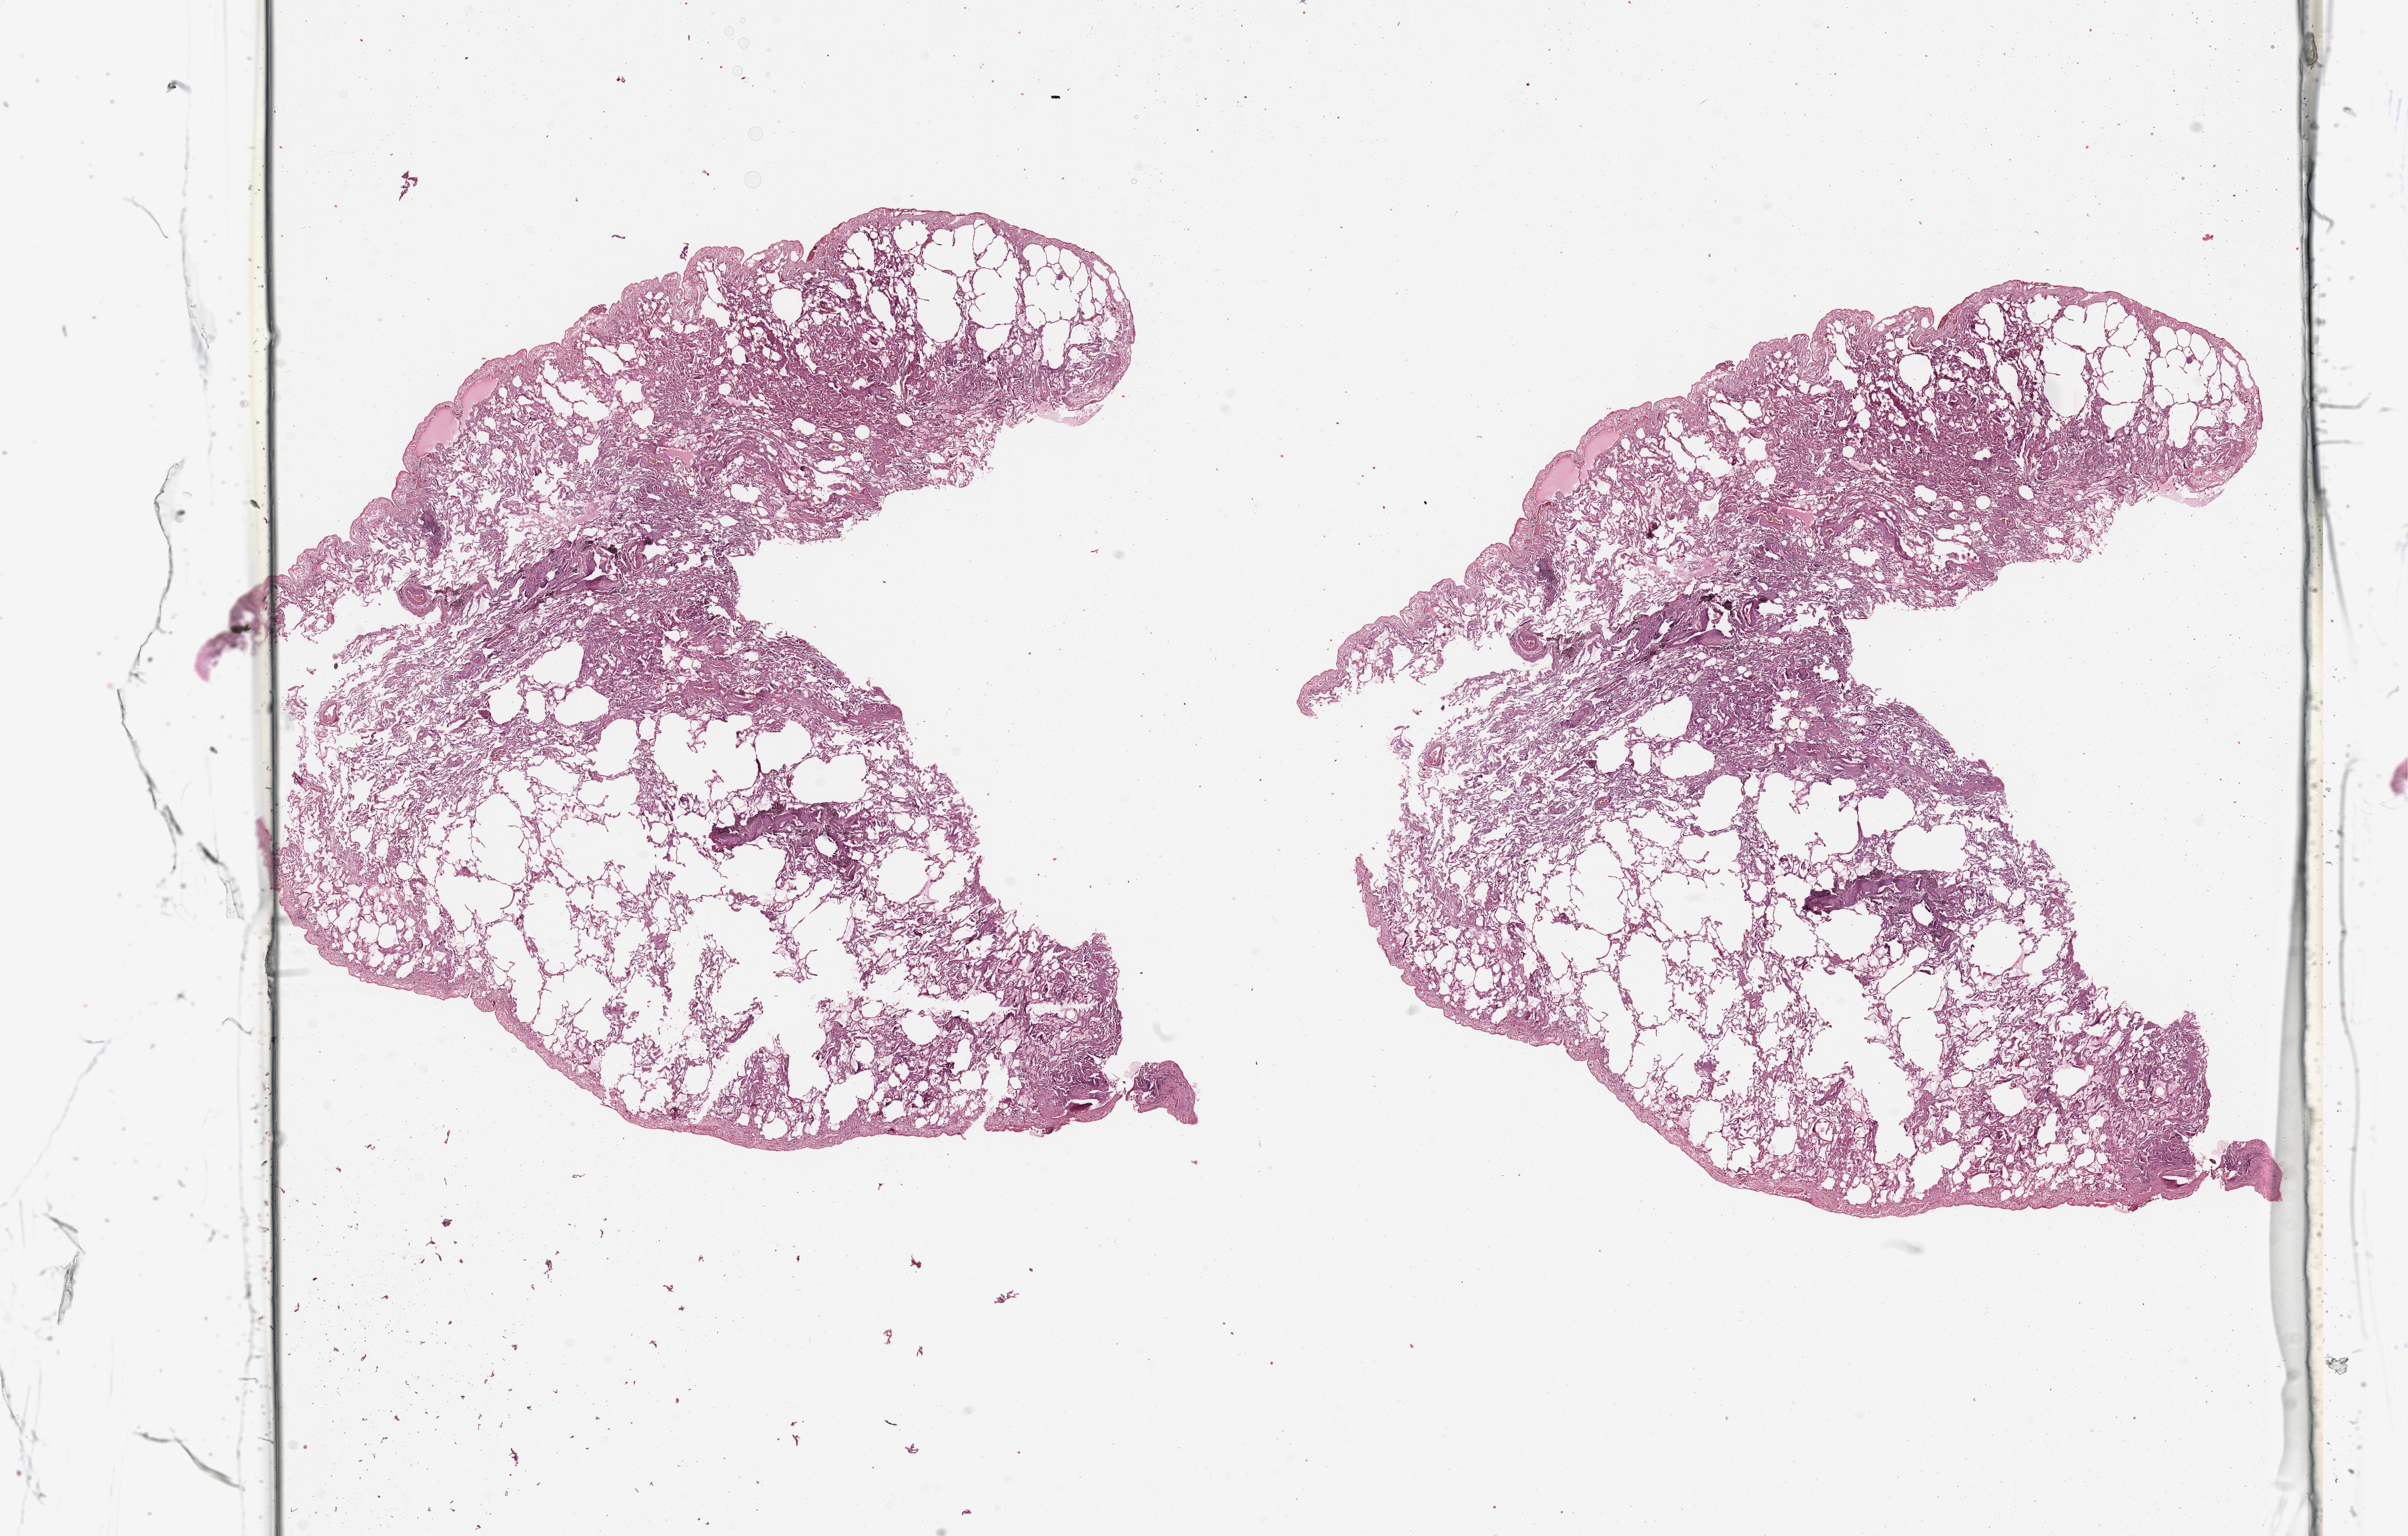
H&E whole-slide image, shown as a low-resolution overview of the whole scanned area (about 28.5 x 18.2 mm); normal (non-tumour) tissue sample, sampled site: lung. Patient: female, age 73 years.
• this section: normal (non-tumour) tissue from the same patient
• patient diagnosis: Adenocarcinoma, NOS